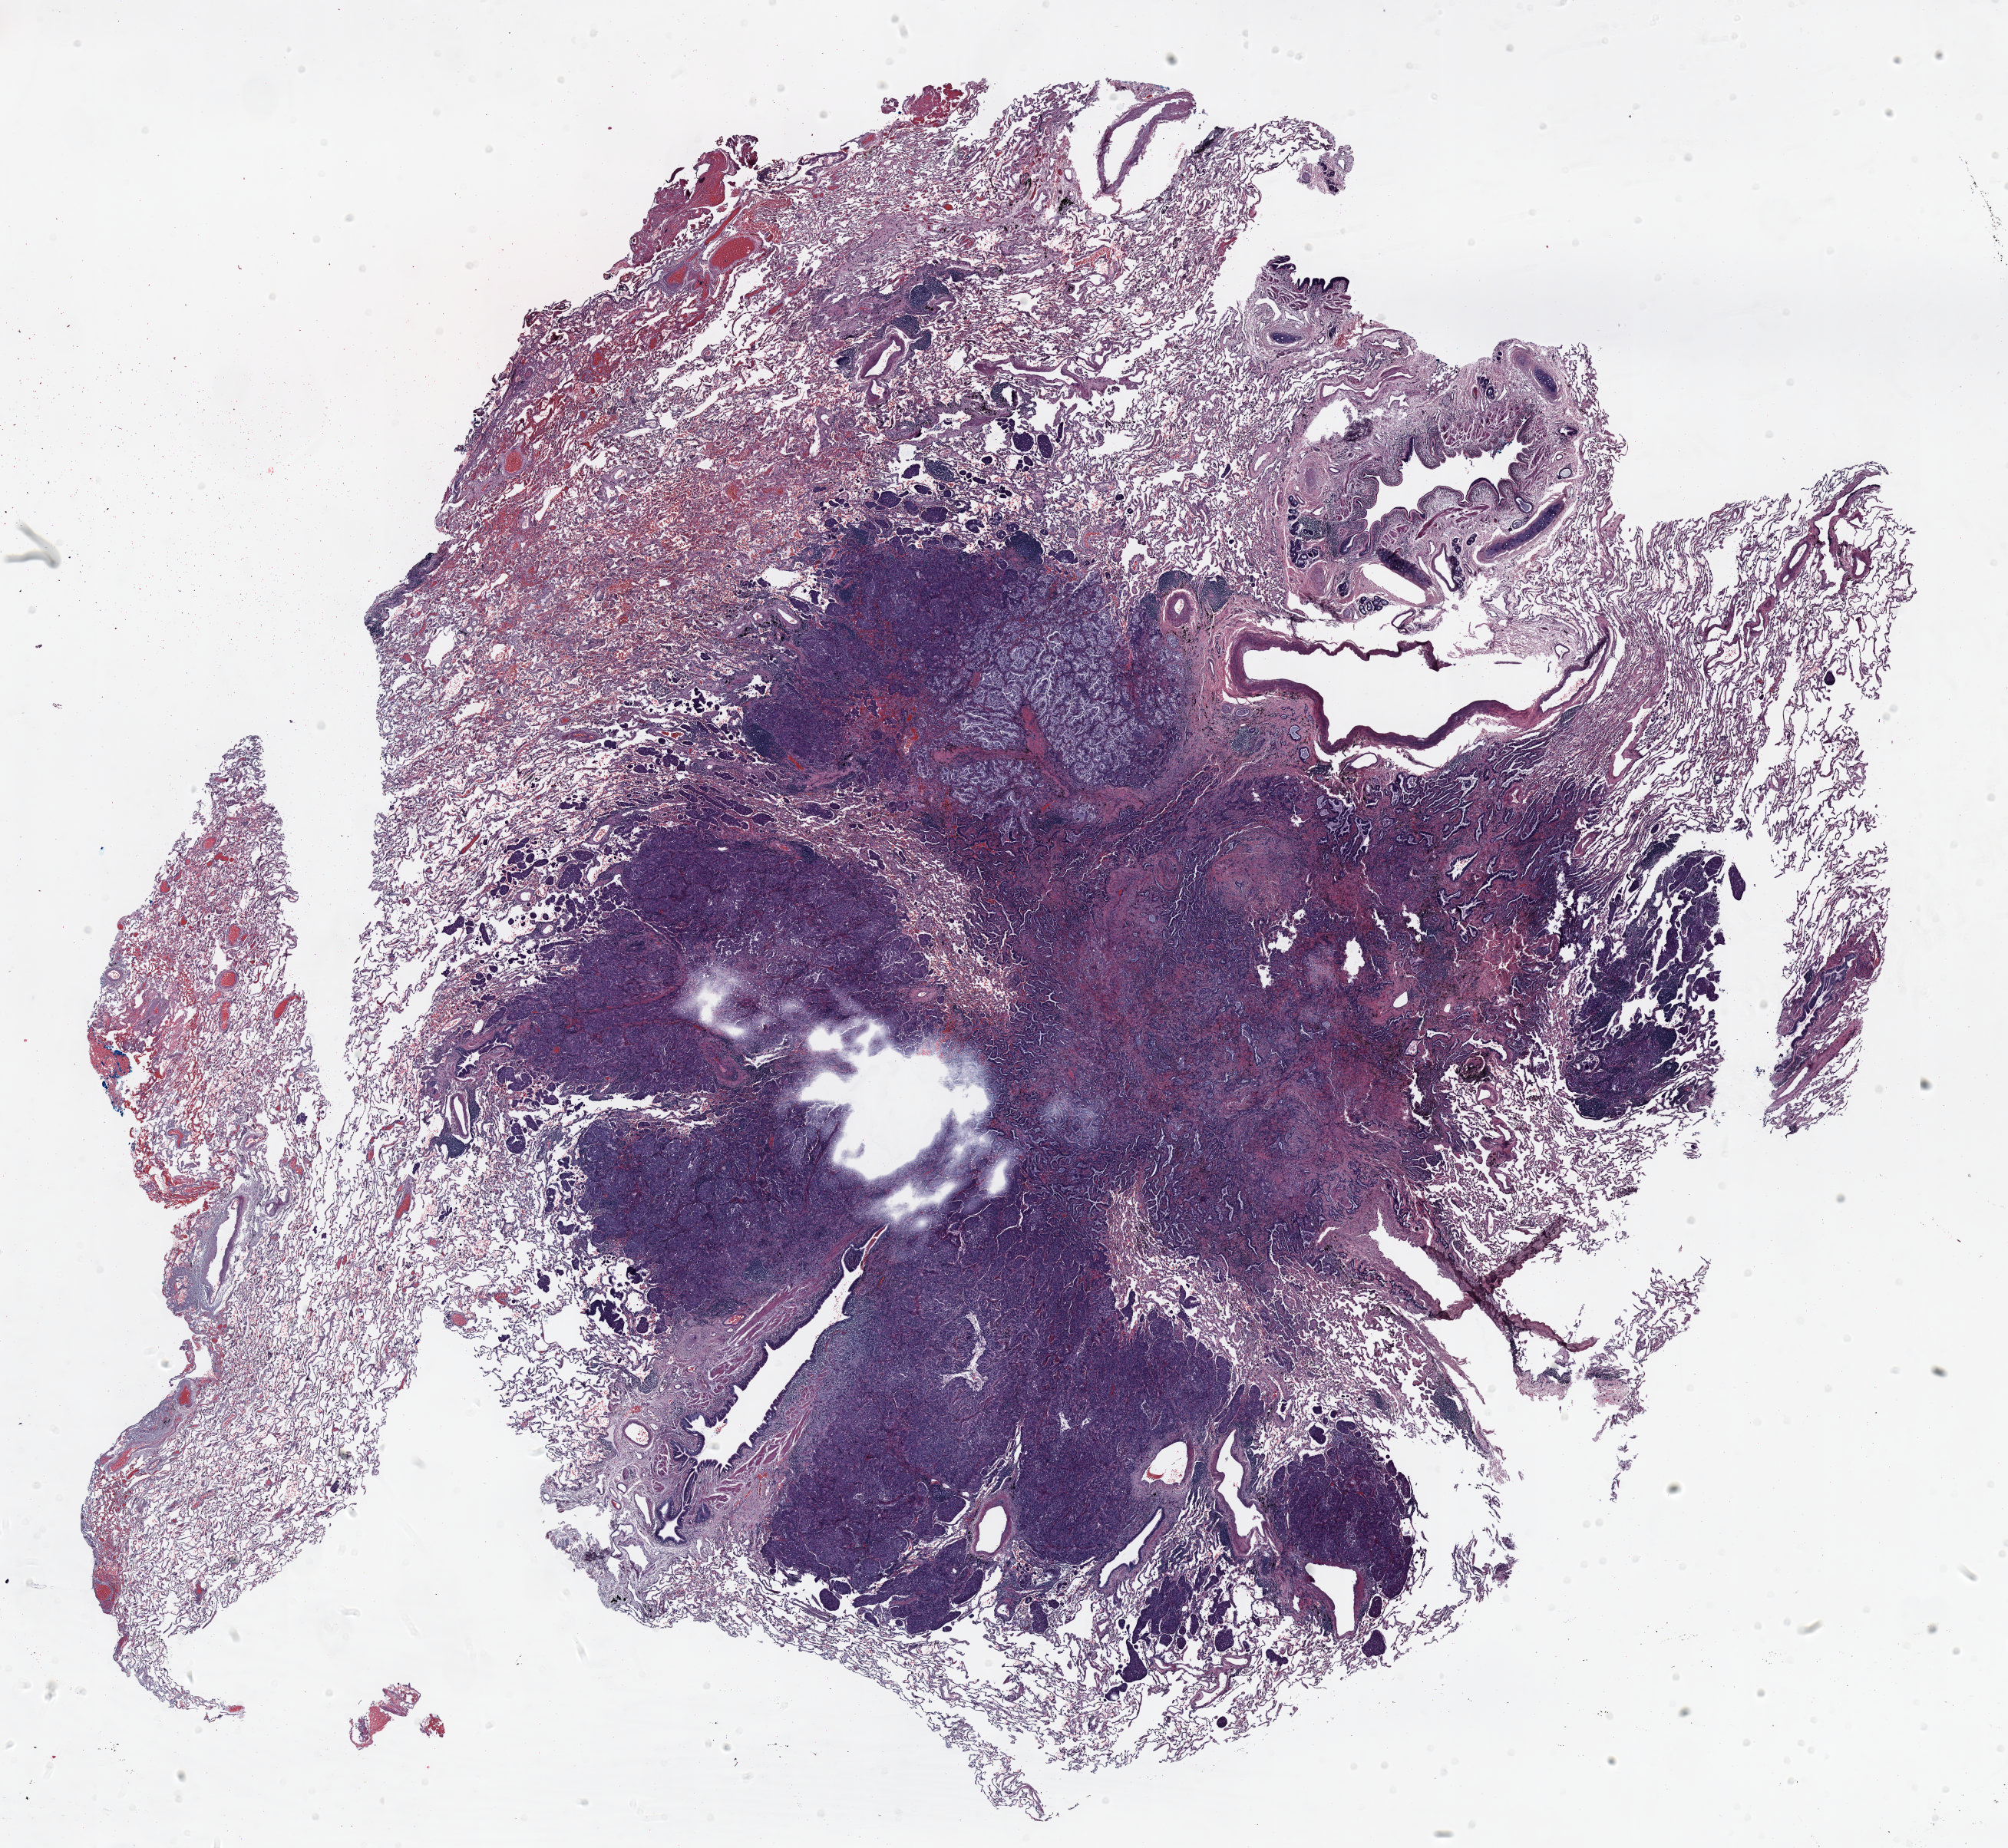
Whole-slide histology image, H&E — shown as a low-resolution overview of the whole scanned area (about 21.0 x 19.3 mm, from a 20x scan). FFPE section. Lung tissue. Male patient, aged 65 at enrolment. Current smoker at enrolment. Grade: poorly differentiated (G3).
Stage (AJCC 6th edition): IA. Primary tumour location (clinical record): right lower lobe. Tumour size (pathology): 18 mm. Participant's lung-cancer diagnosis: Adenocarcinoma, NOS (ICD-O-3 8140/3).